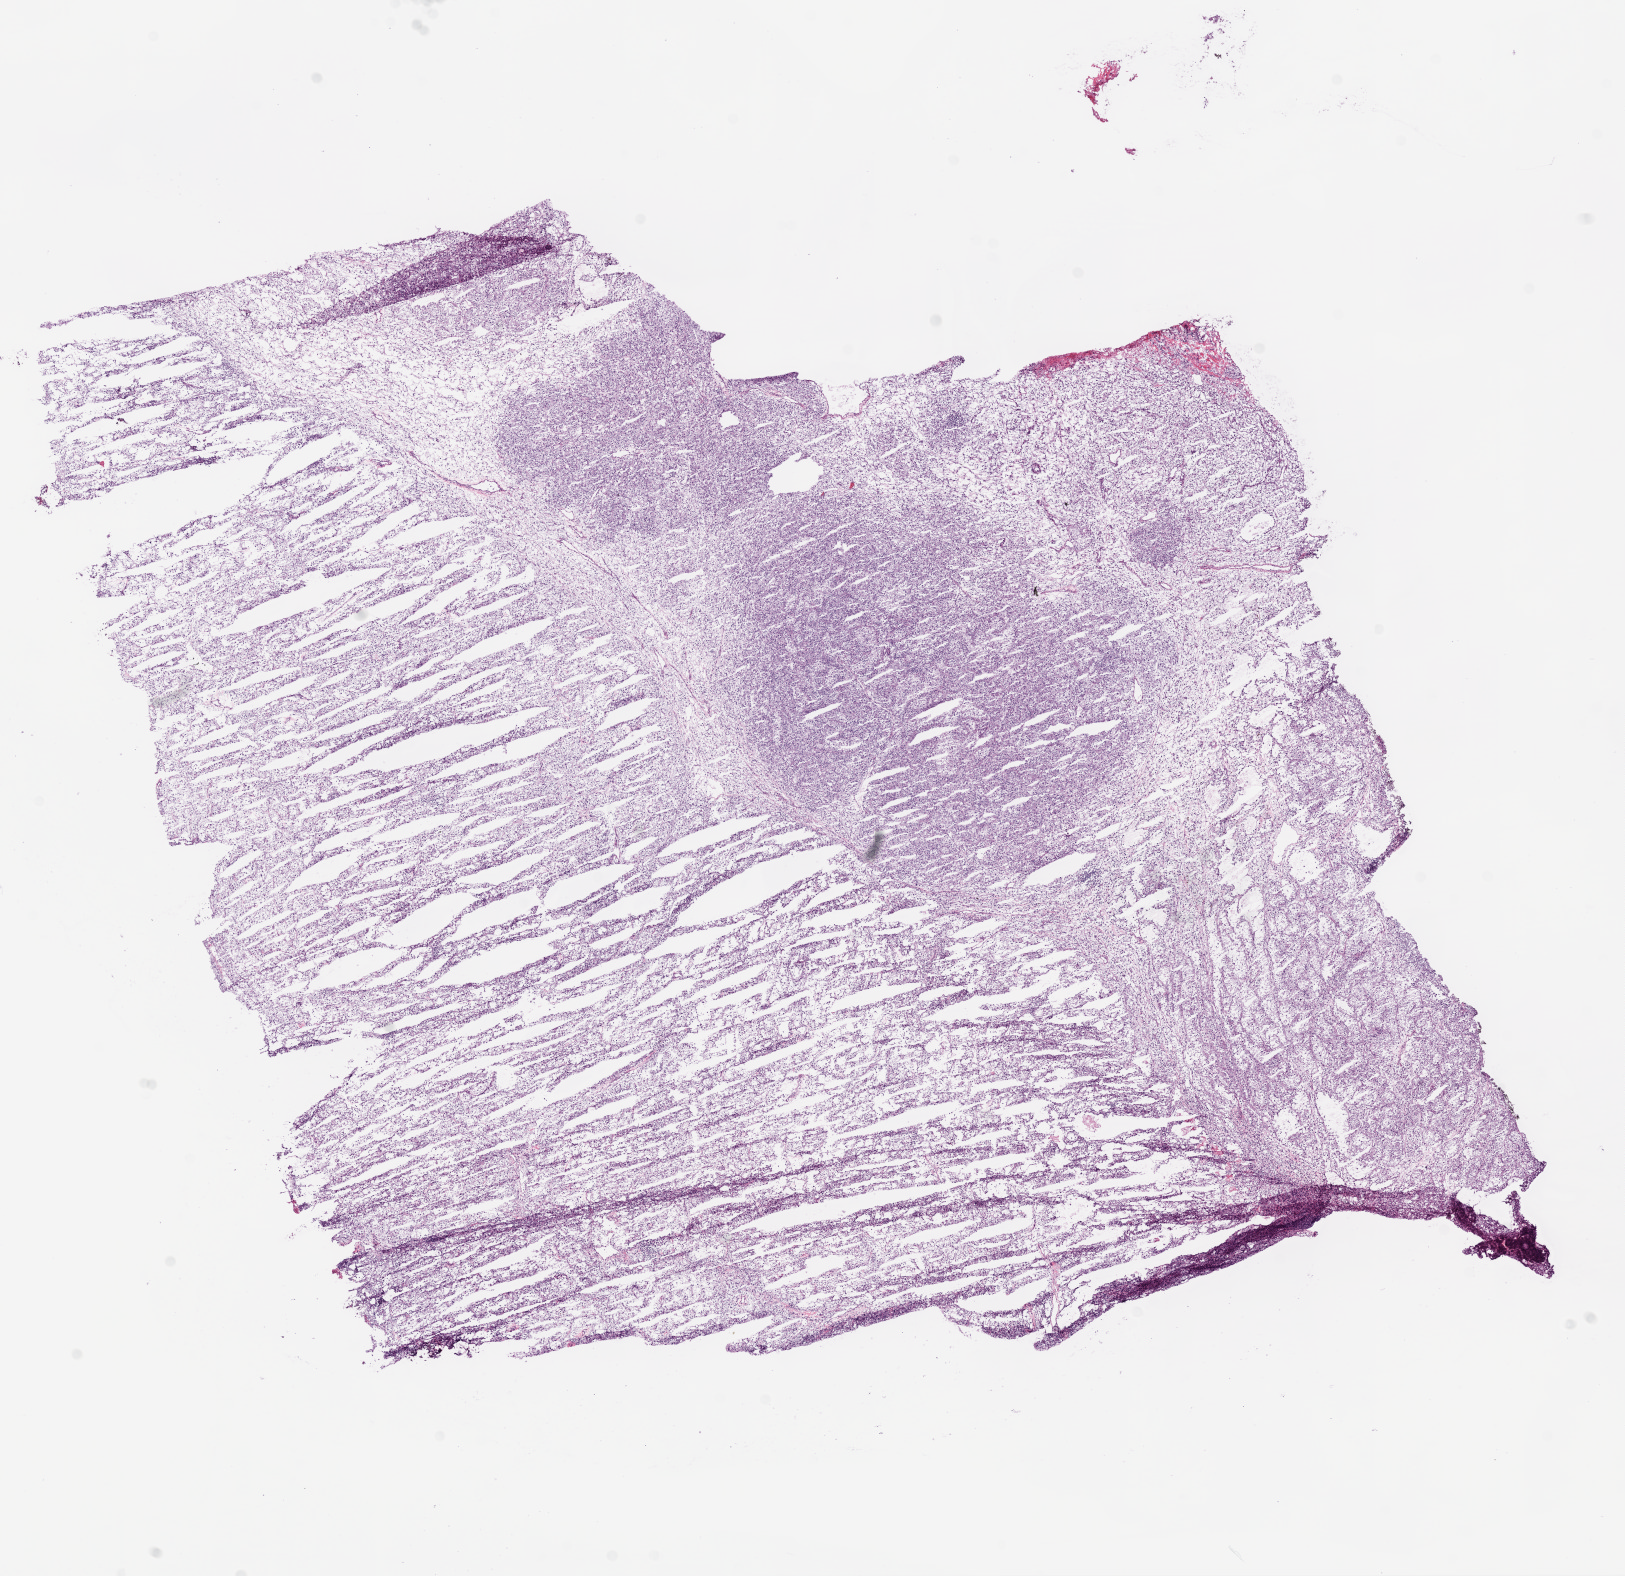
H&E-stained whole-slide image, shown as a low-resolution overview of the whole scanned area (about 13.0 x 12.6 mm); frozen section; primary tumour sample from the kidney. Male patient; age at initial diagnosis 57 years. Histologic grade: G2 (moderately differentiated). Composition of this section per pathologist review: tumour cells 95%, tumour nuclei 85%, normal cells 0%, stromal cells 5%, necrosis 0%.
* laterality: right
* AJCC pathologic stage: I
* diagnosis: Clear cell adenocarcinoma, NOS
* TNM: T1 NX M0